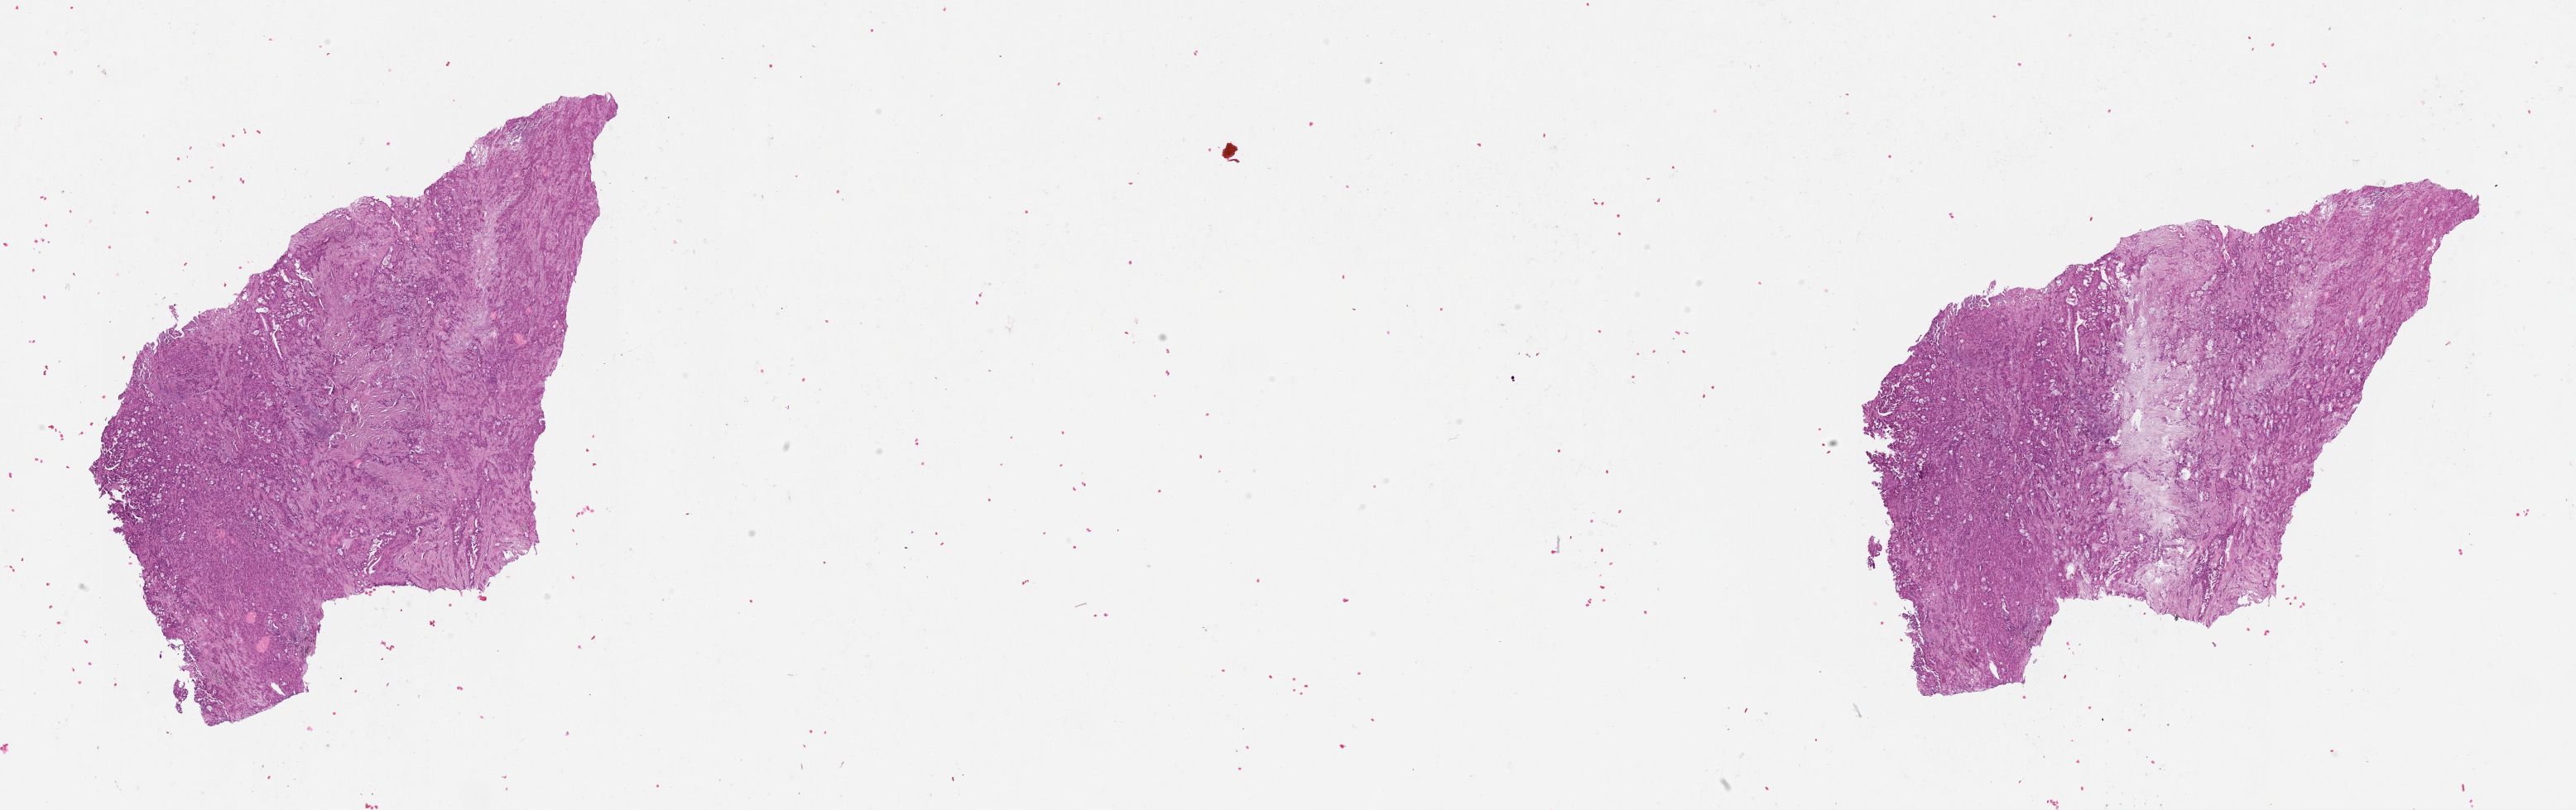
Whole-slide histology image, H&E-stained — shown as a low-resolution overview of the whole scanned area (about 25.1 x 7.9 mm). Tumour tissue sample, lung. 60-year-old female patient.
Patient diagnosis (cohort enrolment): squamous cell carcinoma (lung).